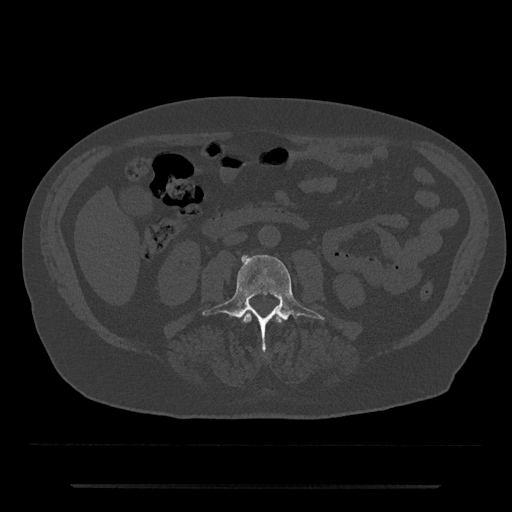
CT including the spine, one axial slice. Slice 417 of 797 in the series (ordered by position). Bone window (W 1800 / L 400 HU). 512 × 512 image matrix, field of view 434 × 434 mm. Male patient, age 80 years. Case-level facts recorded for this patient, not image findings: primary cancer: prostate; vertebrae with lytic lesions (as recorded): L1, T11.
Outlined on this slice (semi-automatic segmentation, software-assisted and operator-edited):
- L2 vertebra: box from (x=244, y=315) to (x=282, y=323) px
- L3 vertebra: (x=202, y=255)–(x=324, y=352)